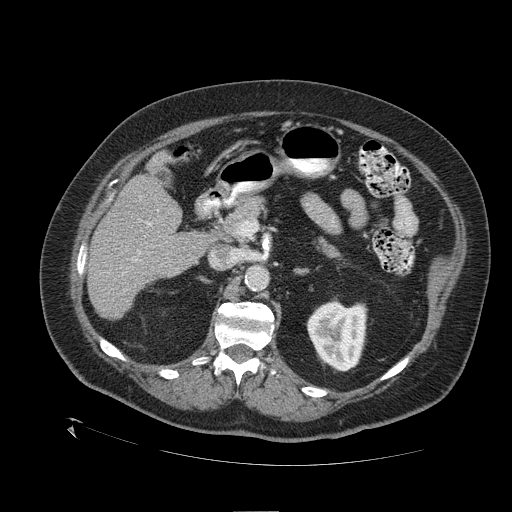
Contrast-enhanced abdominal CT (liver protocol), one axial slice. Slice 59 of 109 in the series (ordered by position). Reconstruction kernel STANDARD. 120 kVp. One of 2 acquisitions stored at this slice position. Soft-tissue window (W 400 / L 40 HU). 512 × 512 image matrix. From the clinical record (not read from this slice): diagnosis: hepatocellular carcinoma (patient treated with transarterial chemoembolisation; whether this scan precedes or follows treatment is not stated here); TNM stage (as recorded): Stage-I; Child-Pugh class: A; tumour differentiation: no biopsy; tumour nodularity: uninodular.
Structures marked on this image (semi-automatic segmentation, software-assisted and operator-edited):
- liver parenchyma outside the tumour (the mass and vessels are separate outlines, so this box may not span the whole liver): bounding box [x1, y1, x2, y2] px = [88, 174, 210, 318]
- liver vessels: [147, 222, 151, 226]